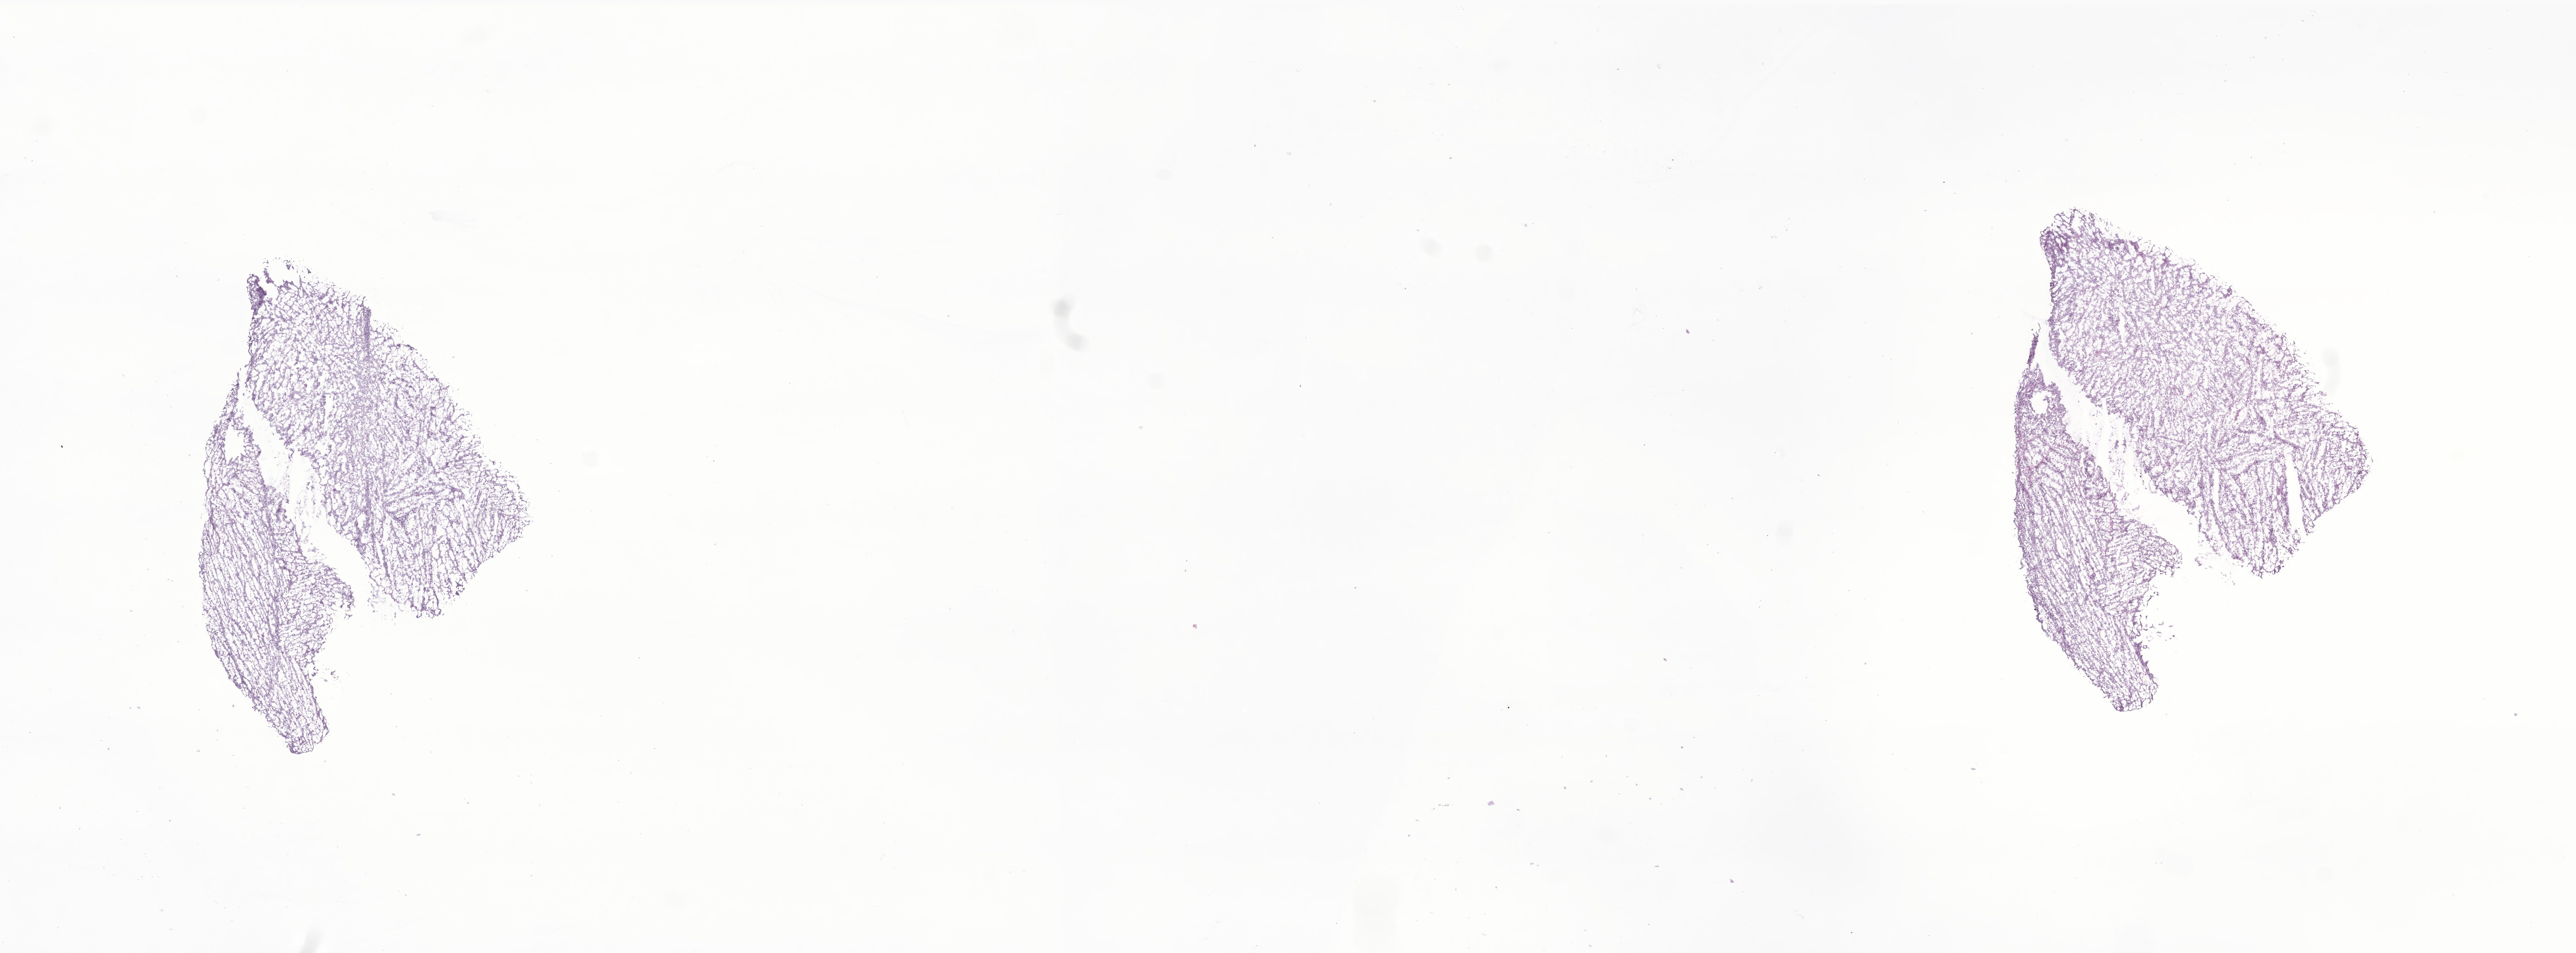
Haematoxylin and eosin whole-slide image of tumor tissue from the testis, a low-resolution overview of the entire scanned area, about 24.7 x 9.1 mm; frozen section. Male patient, age 49 months (4 years 1 month).
* diagnosis: Rhabdomyosarcoma, NOS